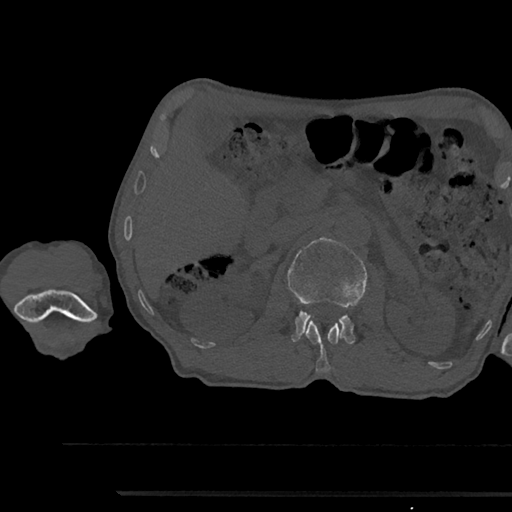
CT including the spine, one axial slice. Slice 600 of 797 in the series (ordered by position). Reconstruction kernel Br40s/3. 120 kVp. Bone window (W 1800 / L 400 HU). 0.5 mm slice thickness. 512 × 512 image matrix, field of view 367 × 367 mm. Patient: male, 79 years. Case-level facts recorded for this patient, not image findings: primary cancer: prostate.
Outlined on this slice (semi-automatically segmented with operator editing):
- L1 vertebra: bounding box (x1, y1, x2, y2) in pixels: (305, 321, 343, 372)
- L2 vertebra: (288, 238, 368, 345)